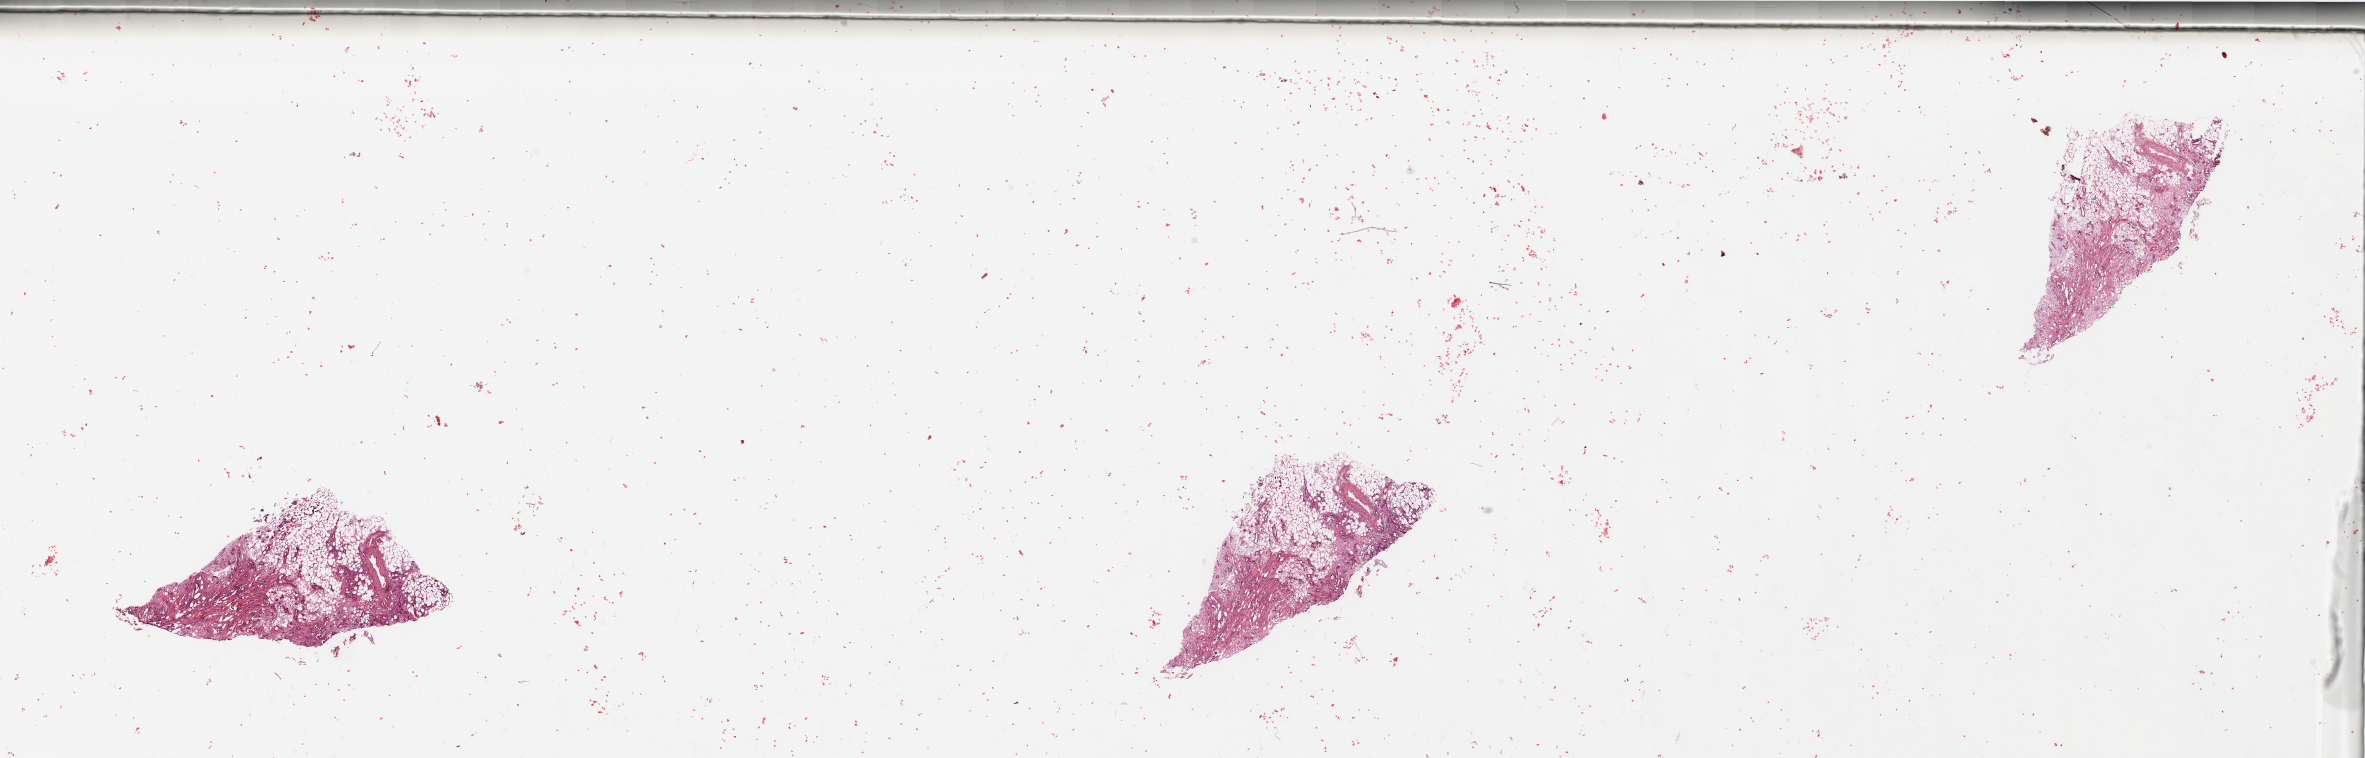
Digitized Hematoxylin and eosin (H&E) stained tissue section (whole slide), shown as a low-resolution overview of the whole scanned area (about 37.4 x 12.0 mm, from a 20x scan), tumour tissue sample, sampled site: pancreas. Patient: female, age 63 years. Histologic grade: G2 (moderately differentiated). Pathologist review of this section (percent, as recorded): tumour nuclei 20%, necrosis 2%.
Histologic diagnosis: Infiltrating duct carcinoma, NOS. AJCC pathologic stage: IIB. Primary tumour site (as recorded): head.